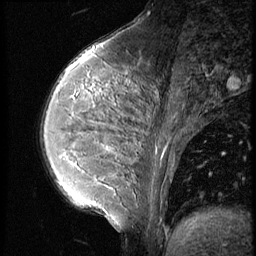
Breast MRI (dynamic contrast-enhanced), one sagittal slice; position 20 of 56 along the scan axis; 3 images stored at this slice position (order not interpretable as contrast timing); 1.5 T; TE 4.2 ms, TR 9 ms; 256 × 256 image matrix, field of view 180 × 180 mm. Patient: female, 35 years. Case-level facts recorded for this patient, not image findings: setting: breast cancer imaged before/during neoadjuvant chemotherapy; receptor status: HR-positive, HER2-negative.
Outlined on this slice (semi-automatically segmented with operator editing):
- analysis volume of interest (the breast-tissue region the enhancement analysis was run in; not a lesion): bounding box <63,60,190,218> (left, top, right, bottom; pixels)
- tumour enhancement mask (voxels above the 140 % enhancement threshold inside the analysis volume of interest): <67,64,110,183>